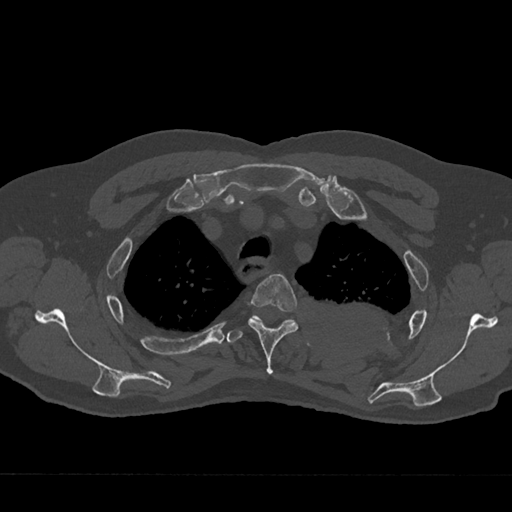
CT including the spine, one axial slice. Position 558 of 797 along the scan axis. Reconstruction kernel Br40s/3. 120 kVp. Bone window (W 1800 / L 400 HU). 0.5 mm slice thickness. 512 × 512 image matrix, field of view 377 × 377 mm. Male patient, age 75 years. Case-level facts recorded for this patient, not image findings: primary cancer: renal.
Outlined on this slice (semi-automatically segmented with operator editing):
- T3 vertebra: box from (x=248, y=274) to (x=298, y=375) px
- T4 vertebra: (x=227, y=315)–(x=296, y=343)